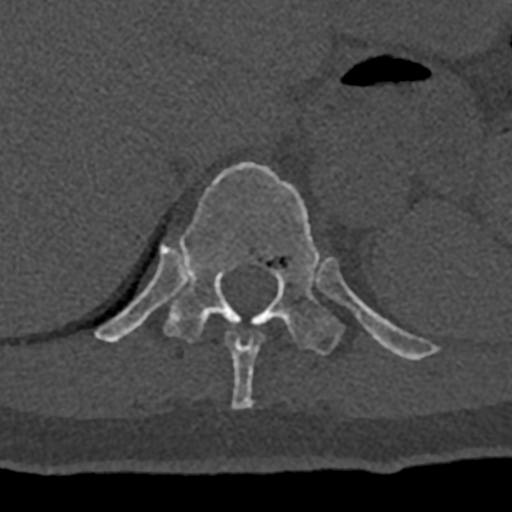
CT including the spine, one axial slice. Position 563 of 797 along the scan axis. Reconstruction kernel Br40s/3. 120 kVp. Bone window (W 1800 / L 400 HU). 0.5 mm slice thickness. 512 × 512 image matrix, field of view 160 × 160 mm. Patient: male, 74 years. Case-level facts recorded for this patient, not image findings: primary cancer: renal; vertebrae with lytic lesions (as recorded): T10, L1, L2, L3, L4, L5.
Outlined on this slice (semi-automatic segmentation, software-assisted and operator-edited):
- T10 vertebra: box from (x=225, y=330) to (x=264, y=409) px
- T11 vertebra: (x=94, y=162)–(x=432, y=361)